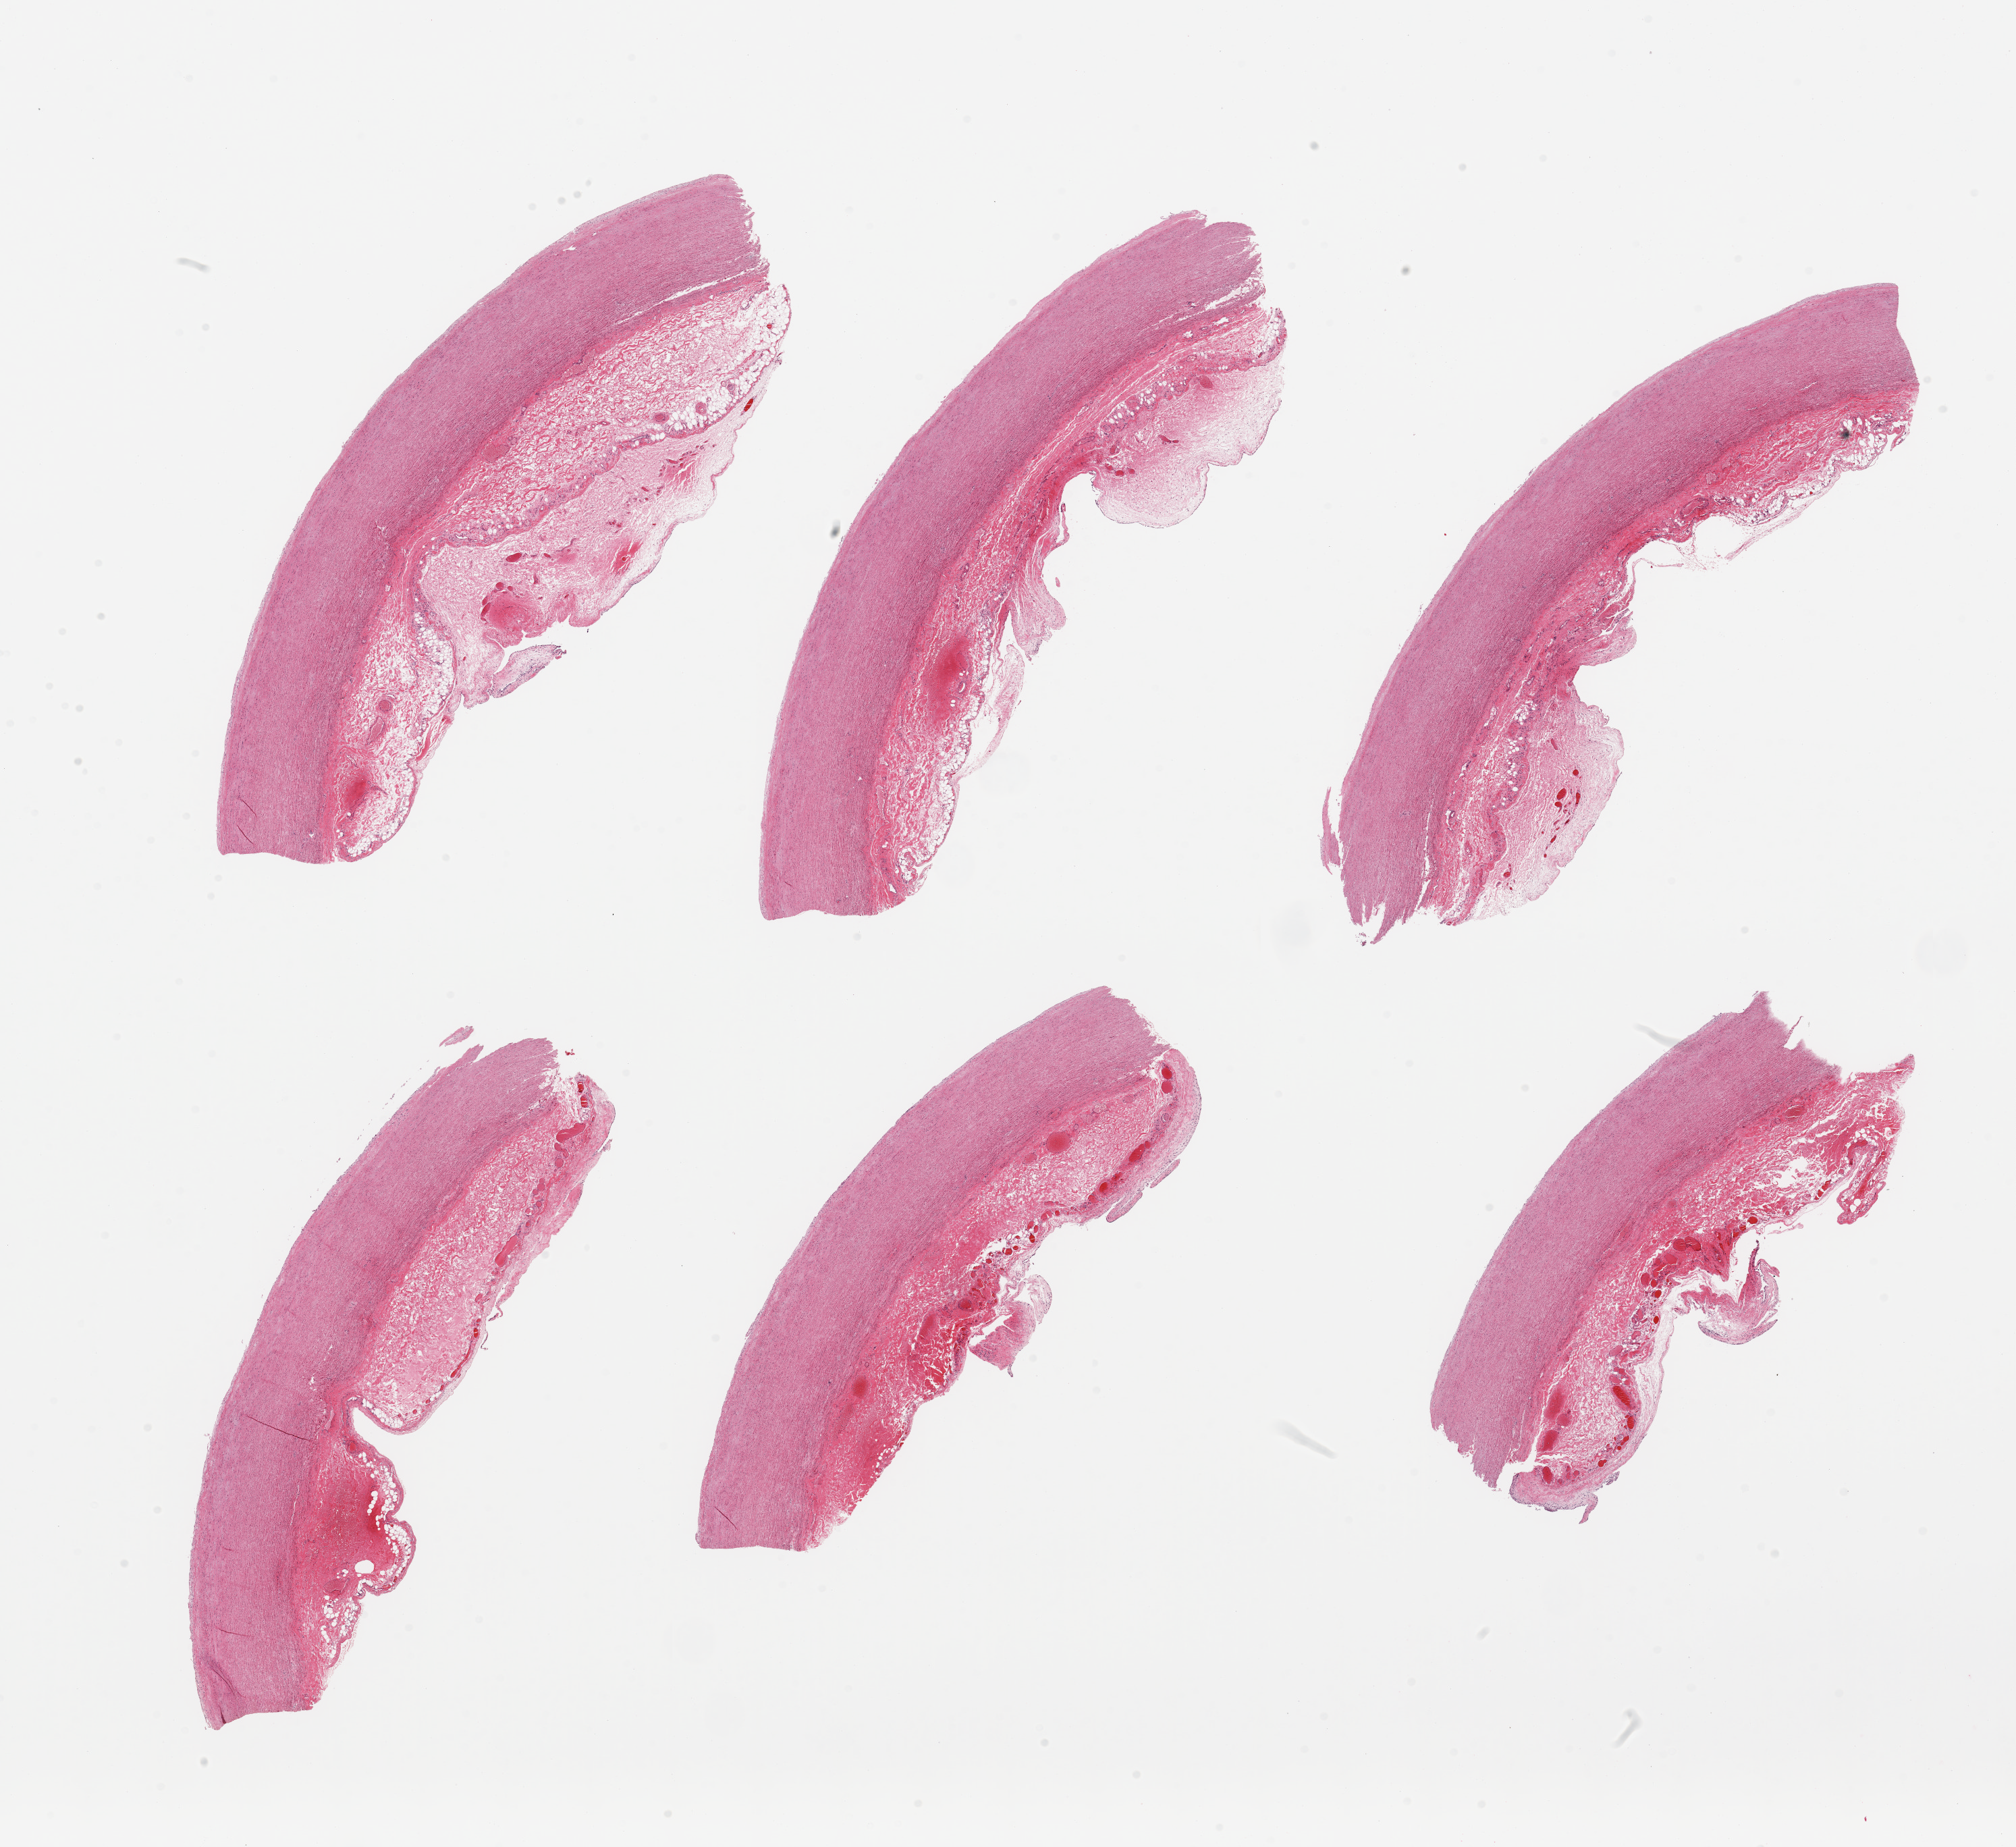
Haematoxylin and eosin whole-slide image, a low-resolution overview of the entire scanned area, about 23.6 x 21.6 mm. PAXgene-fixed paraffin-embedded (PFPE) section. Target tissue: aorta. Tissue donor sample. Donor: male.
Pathologist's review note for this sample: 2 pieces, adherent layers of serosal fat up to ~2mm, minimal atherosis.